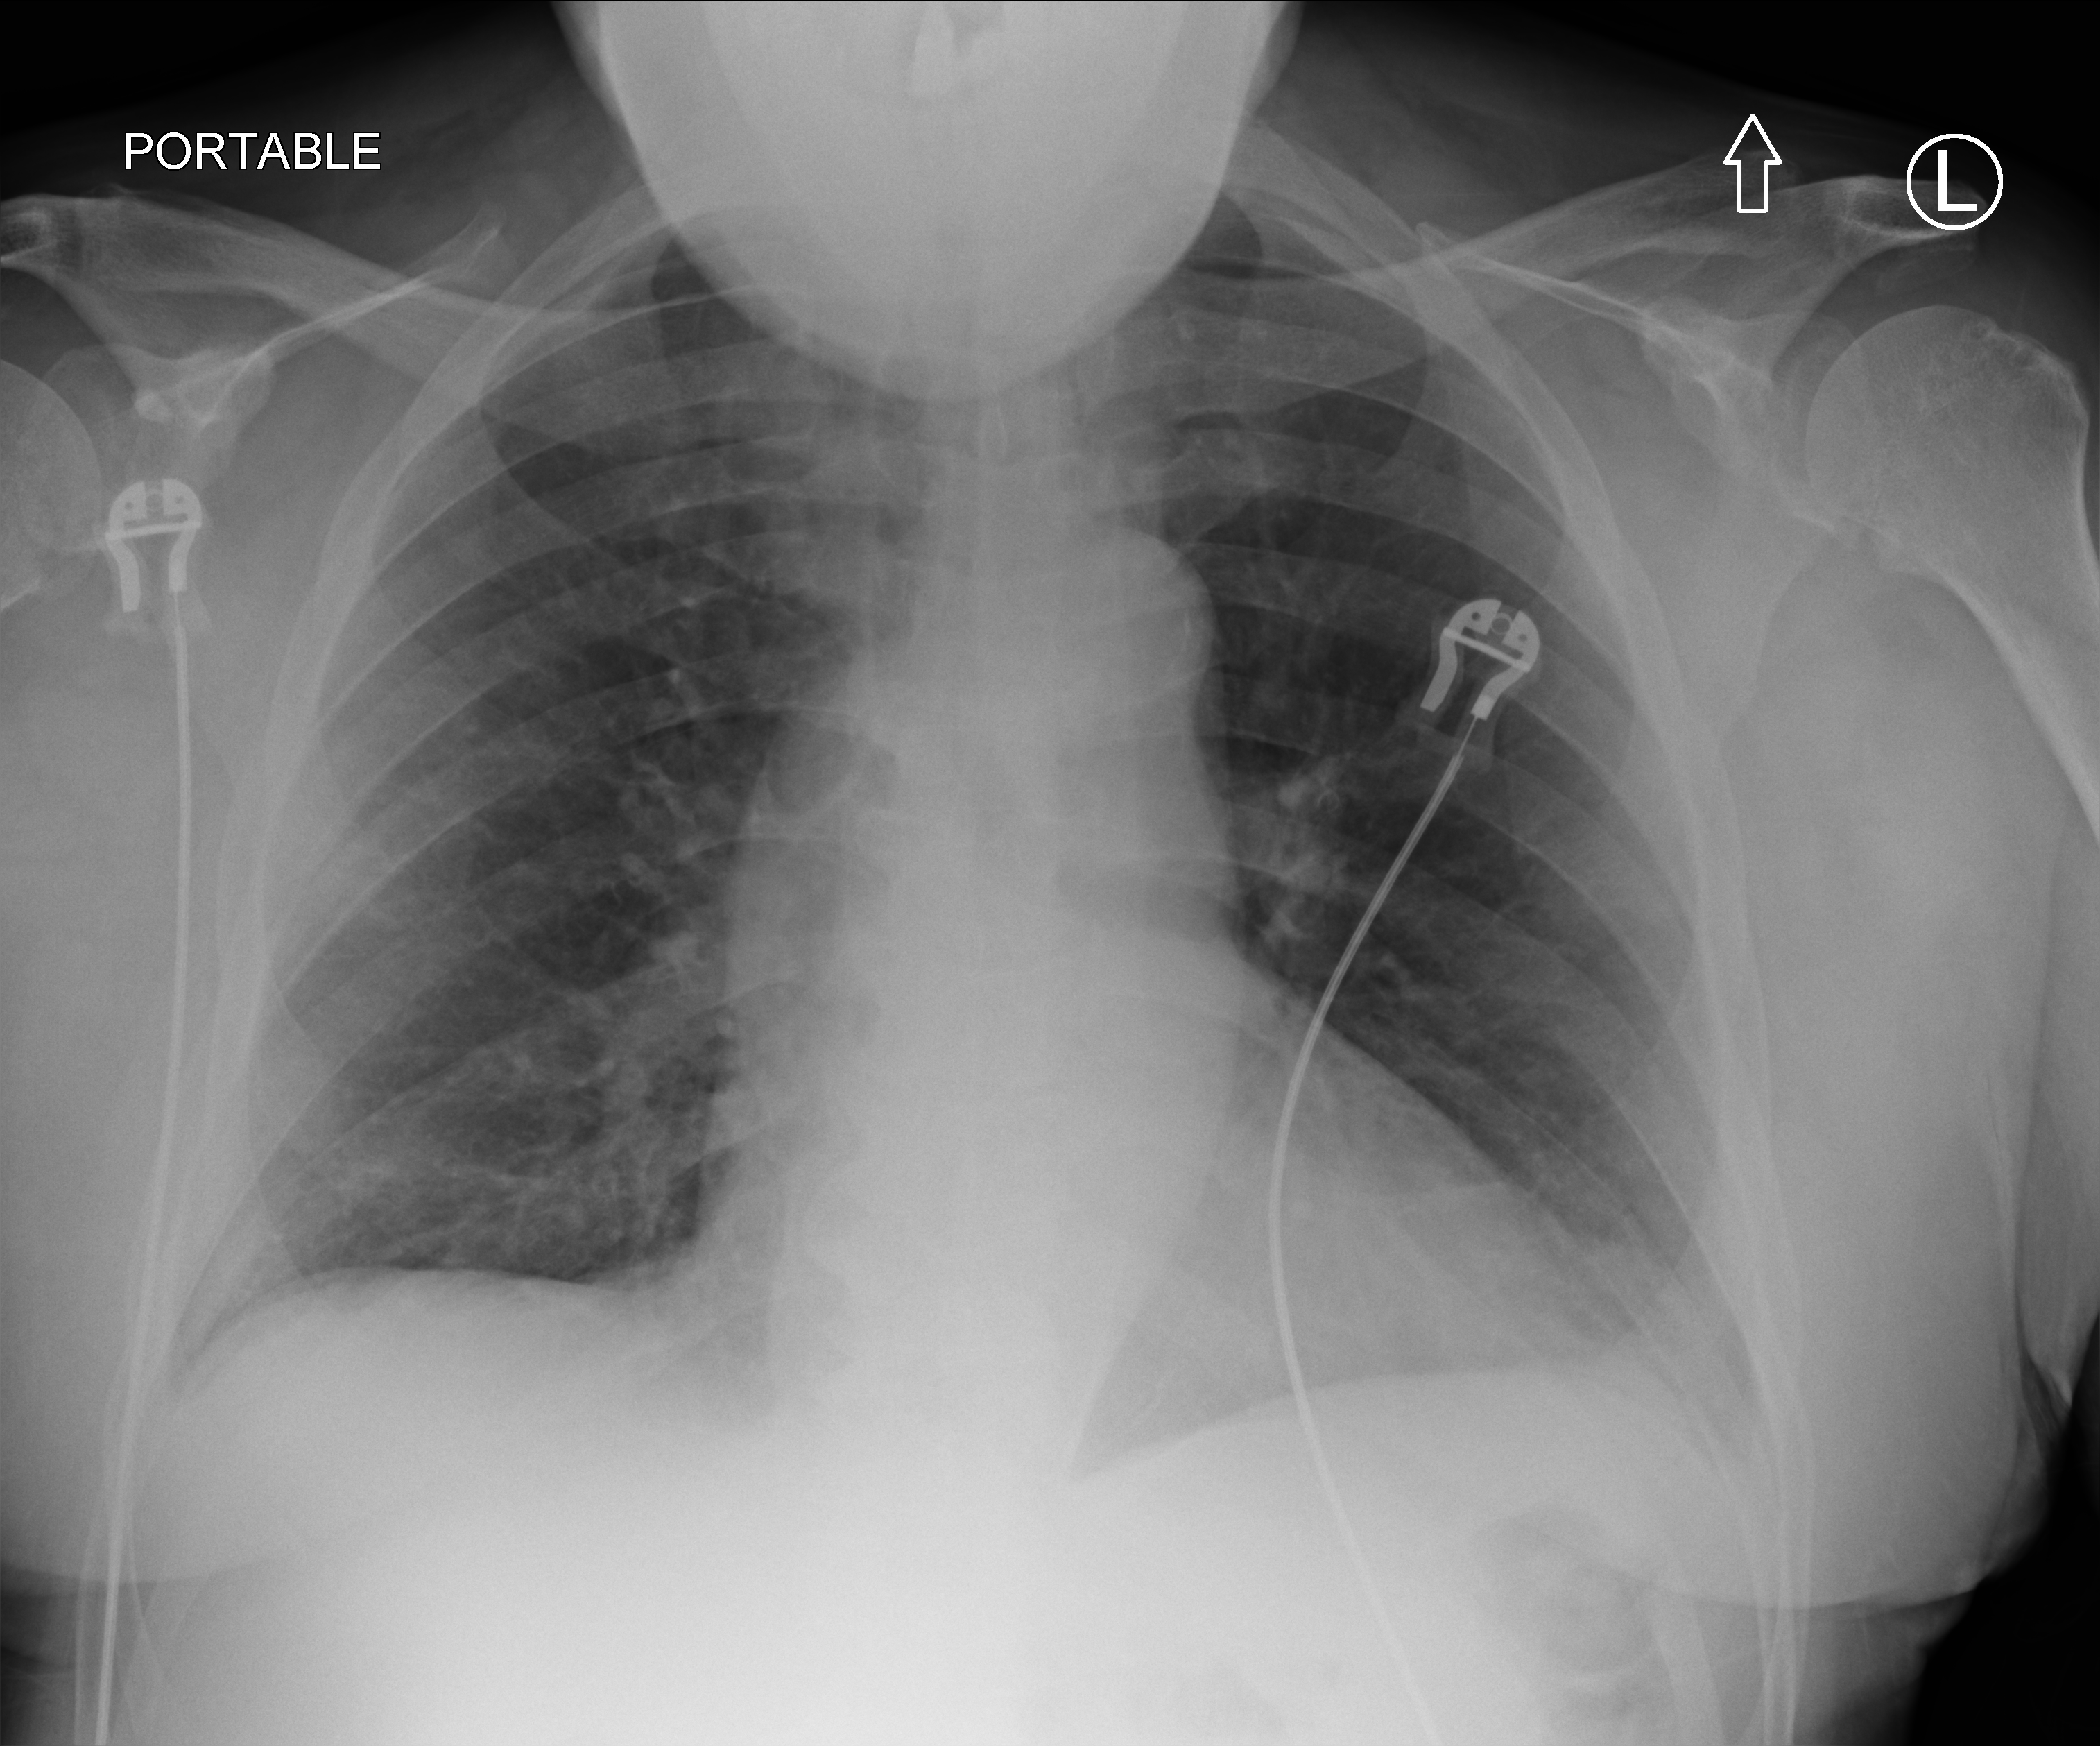
Portable chest radiograph; anteroposterior (AP) projection. Male patient hospitalised with COVID-19, age 60–74 years.
Hospital-stay facts (about this admission, not read from this image; timing relative to this image not recorded): admitted to intensive care during this hospital stay: no; mechanically ventilated during this hospital stay: no.